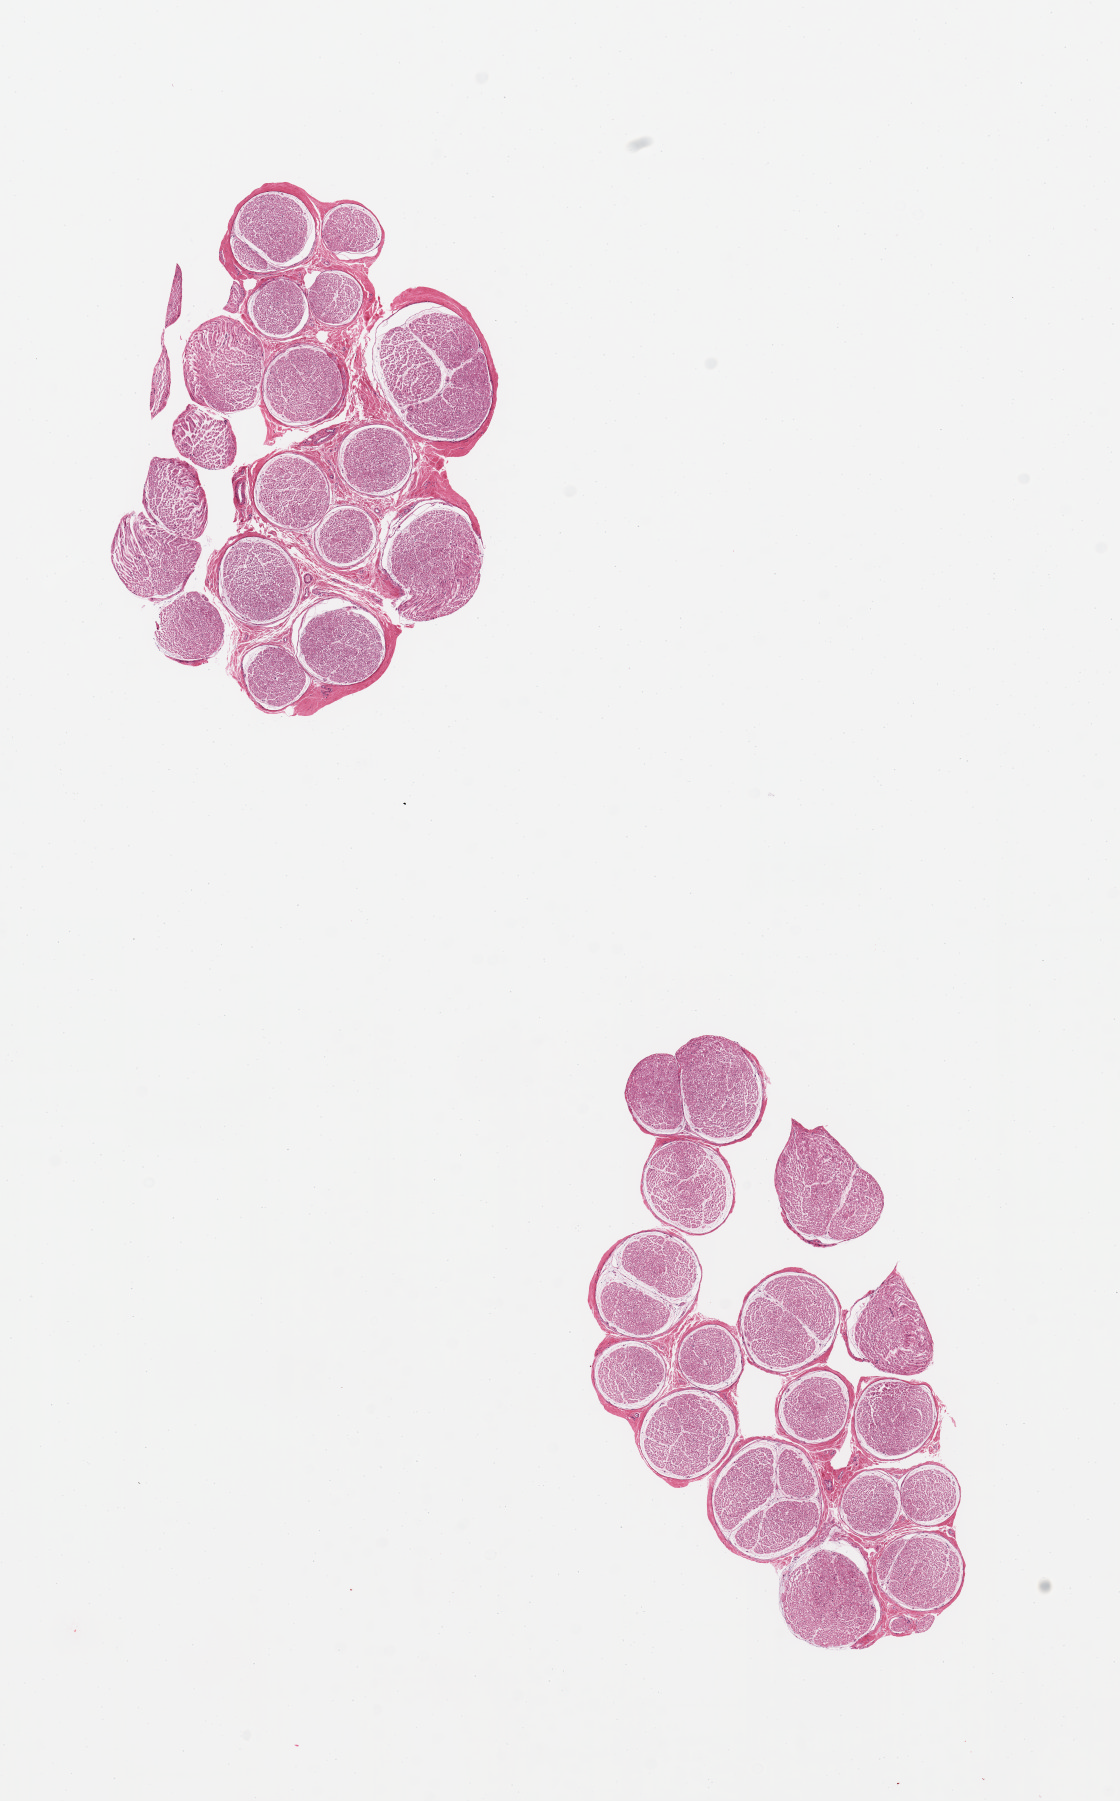
Whole-slide image, haematoxylin and eosin stain, low-resolution overview of the scanned area, about 8.9 x 14.2 mm, PAXgene-fixed paraffin-embedded (PFPE) section, target tissue: tibial nerve, tissue donor sample. Male donor.
* reviewer comment on this tissue sample: 2 pieces, pristine specimen